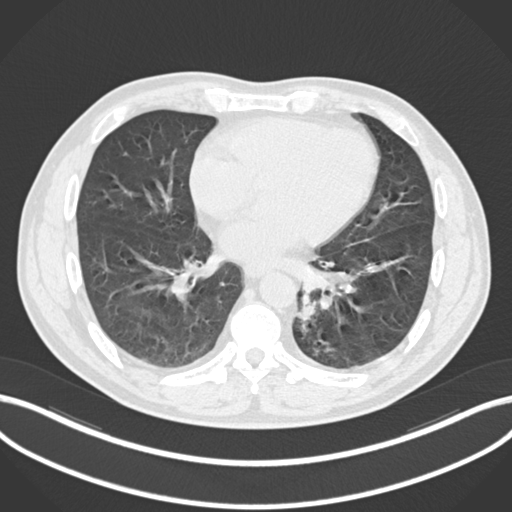
Chest CT, one axial slice; slice 83 of 223 in the series (ordered by position); 120 kVp; lung window (W 1500 / L -600 HU); 1 mm slice thickness; 512 × 512 image matrix, field of view 400 × 400 mm. Patient: male, 50 years. From the clinical record (not read from this slice): clinical TNM (as recorded): T2a N3 M0.
Annotated regions visible in this slice (rectangle marked by the reading radiologist):
- lung tumour (recorded histology: squamous cell carcinoma): bounding box [x1, y1, x2, y2] px = [294, 290, 322, 327]